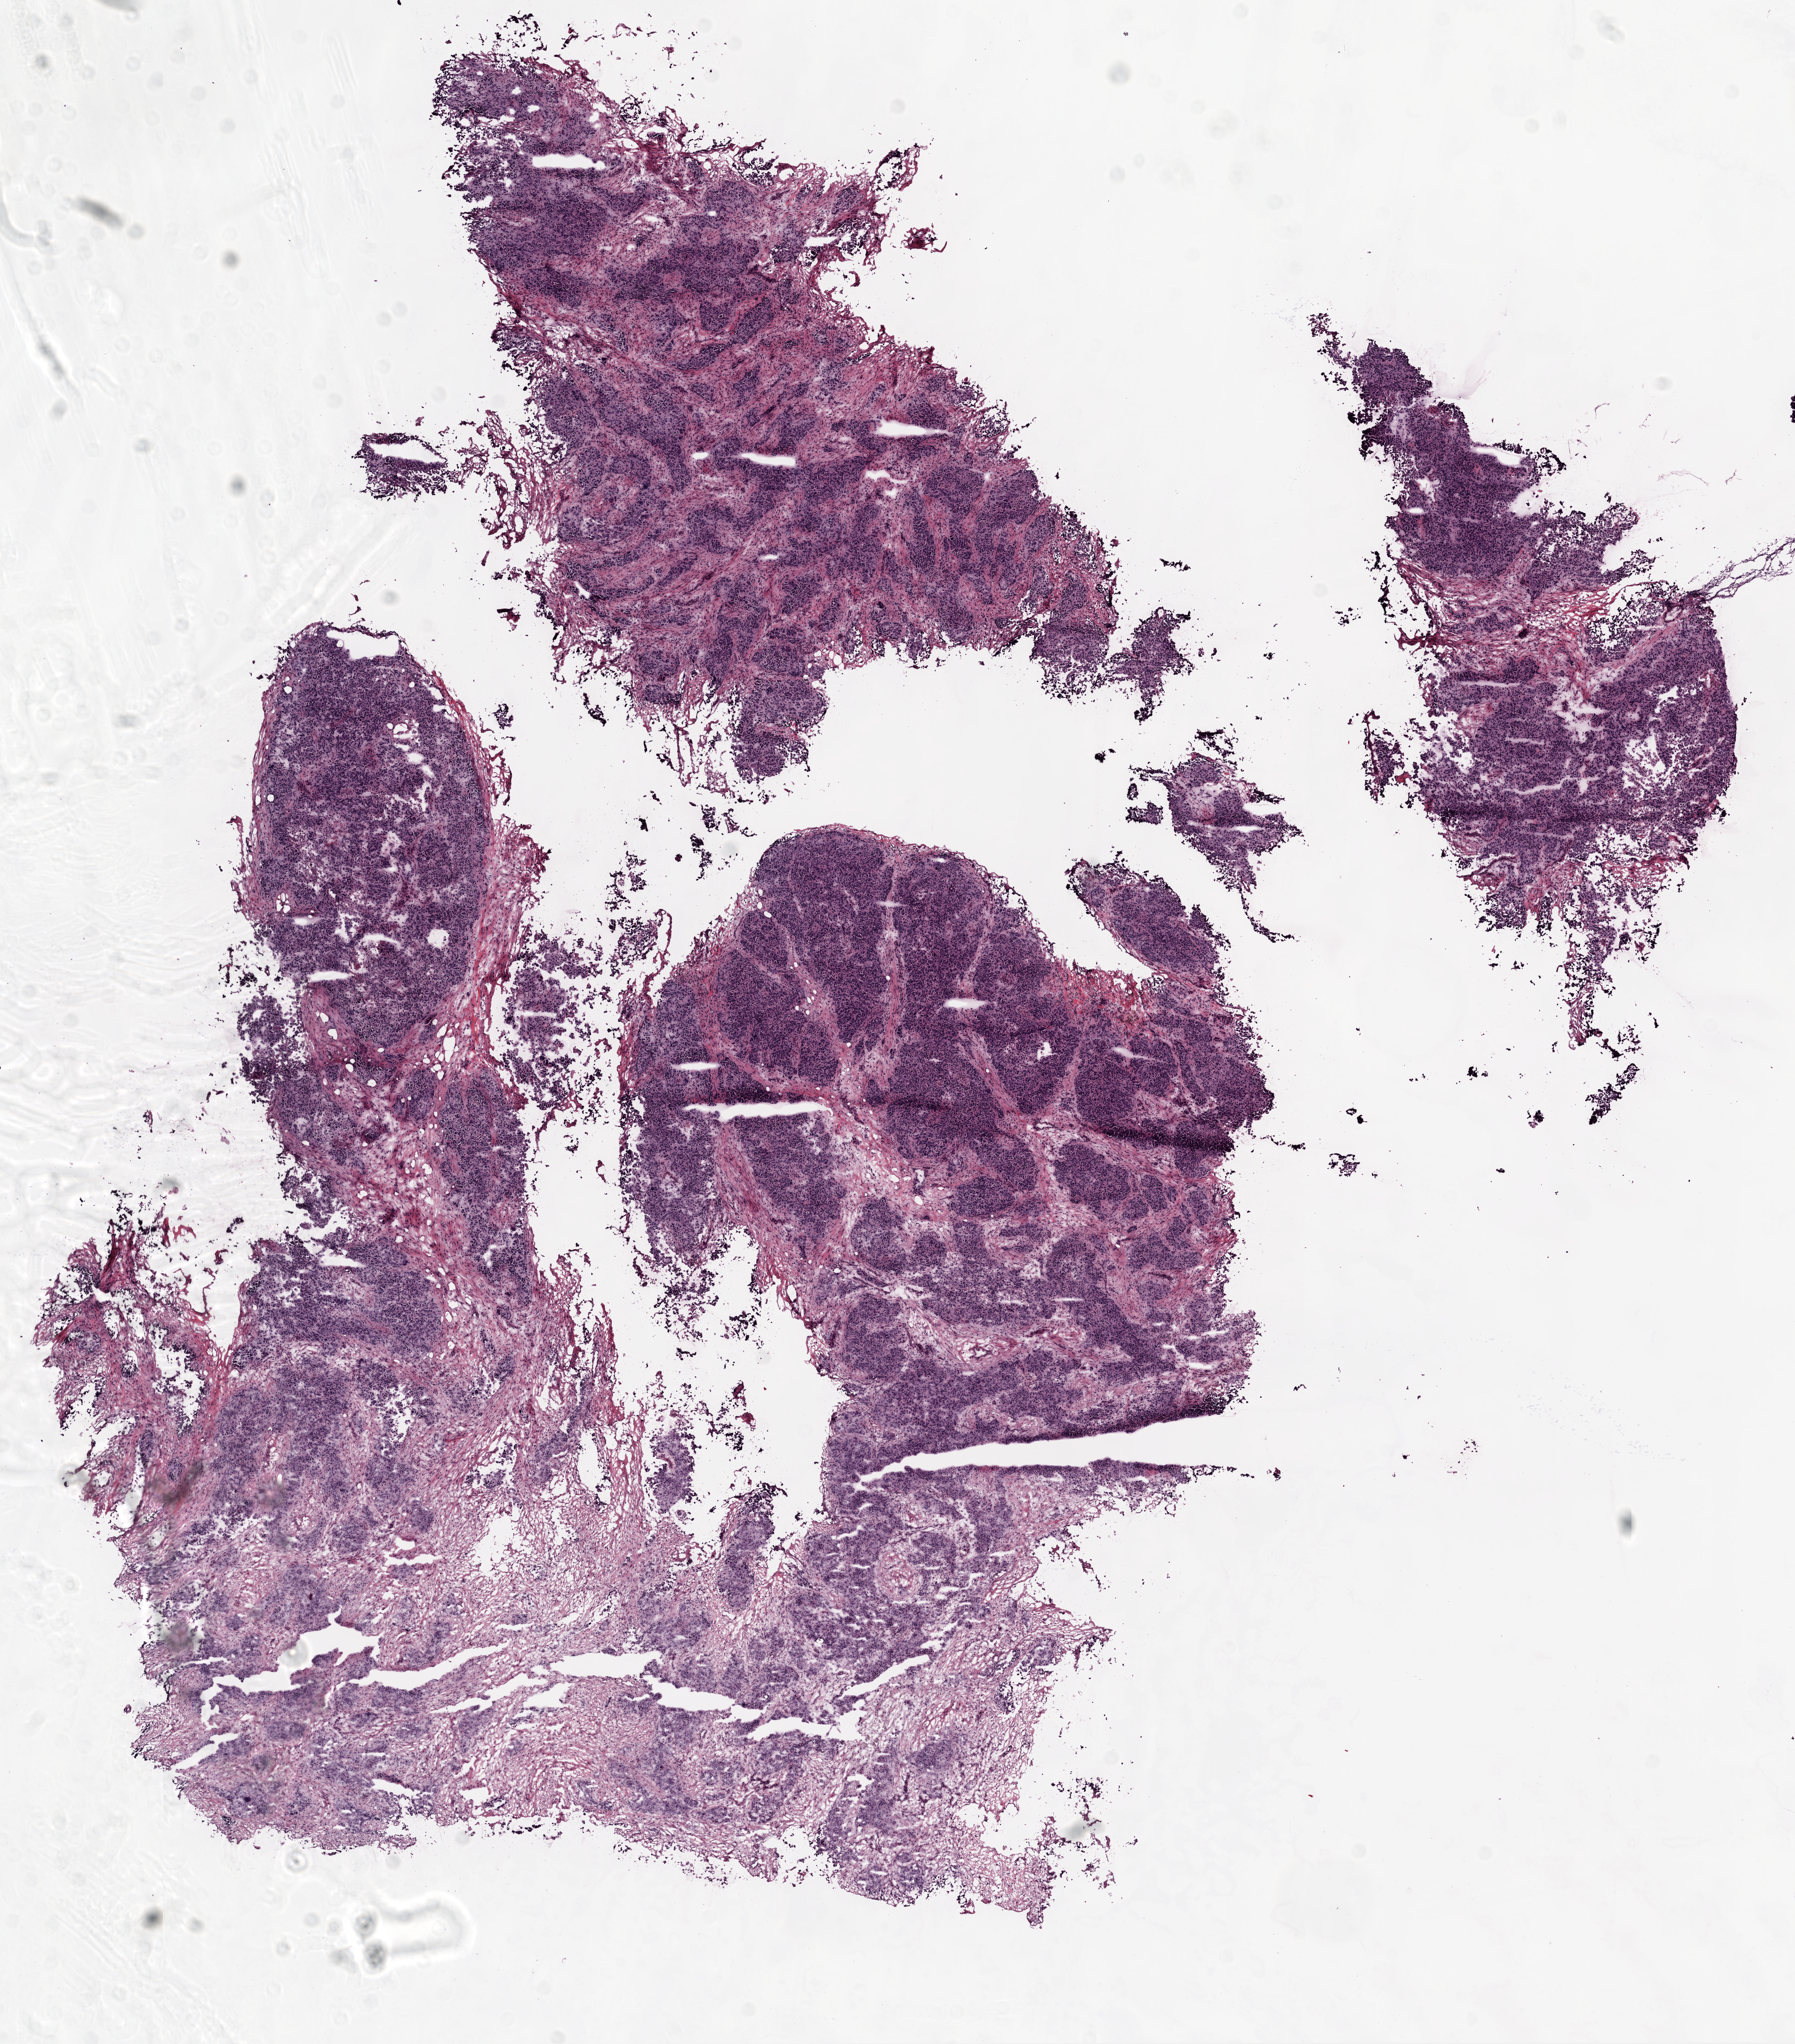
Whole-slide histology image, Hematoxylin and eosin (H&E) stained, a low-resolution overview of the entire scanned area, about 11.0 x 12.6 mm (from a 20x scan). Frozen section from the top of the tissue portion. Sample: primary tumour, ovary. Patient: female, age at initial diagnosis 62 years. Histologic grade: G2 (moderately differentiated). Slide review estimates, as recorded: tumour cells 100%, tumour nuclei 85%, normal cells 0%, stromal cells 0%, necrosis 0%.
* FIGO stage: IIIC
* histologic diagnosis: Serous cystadenocarcinoma, NOS